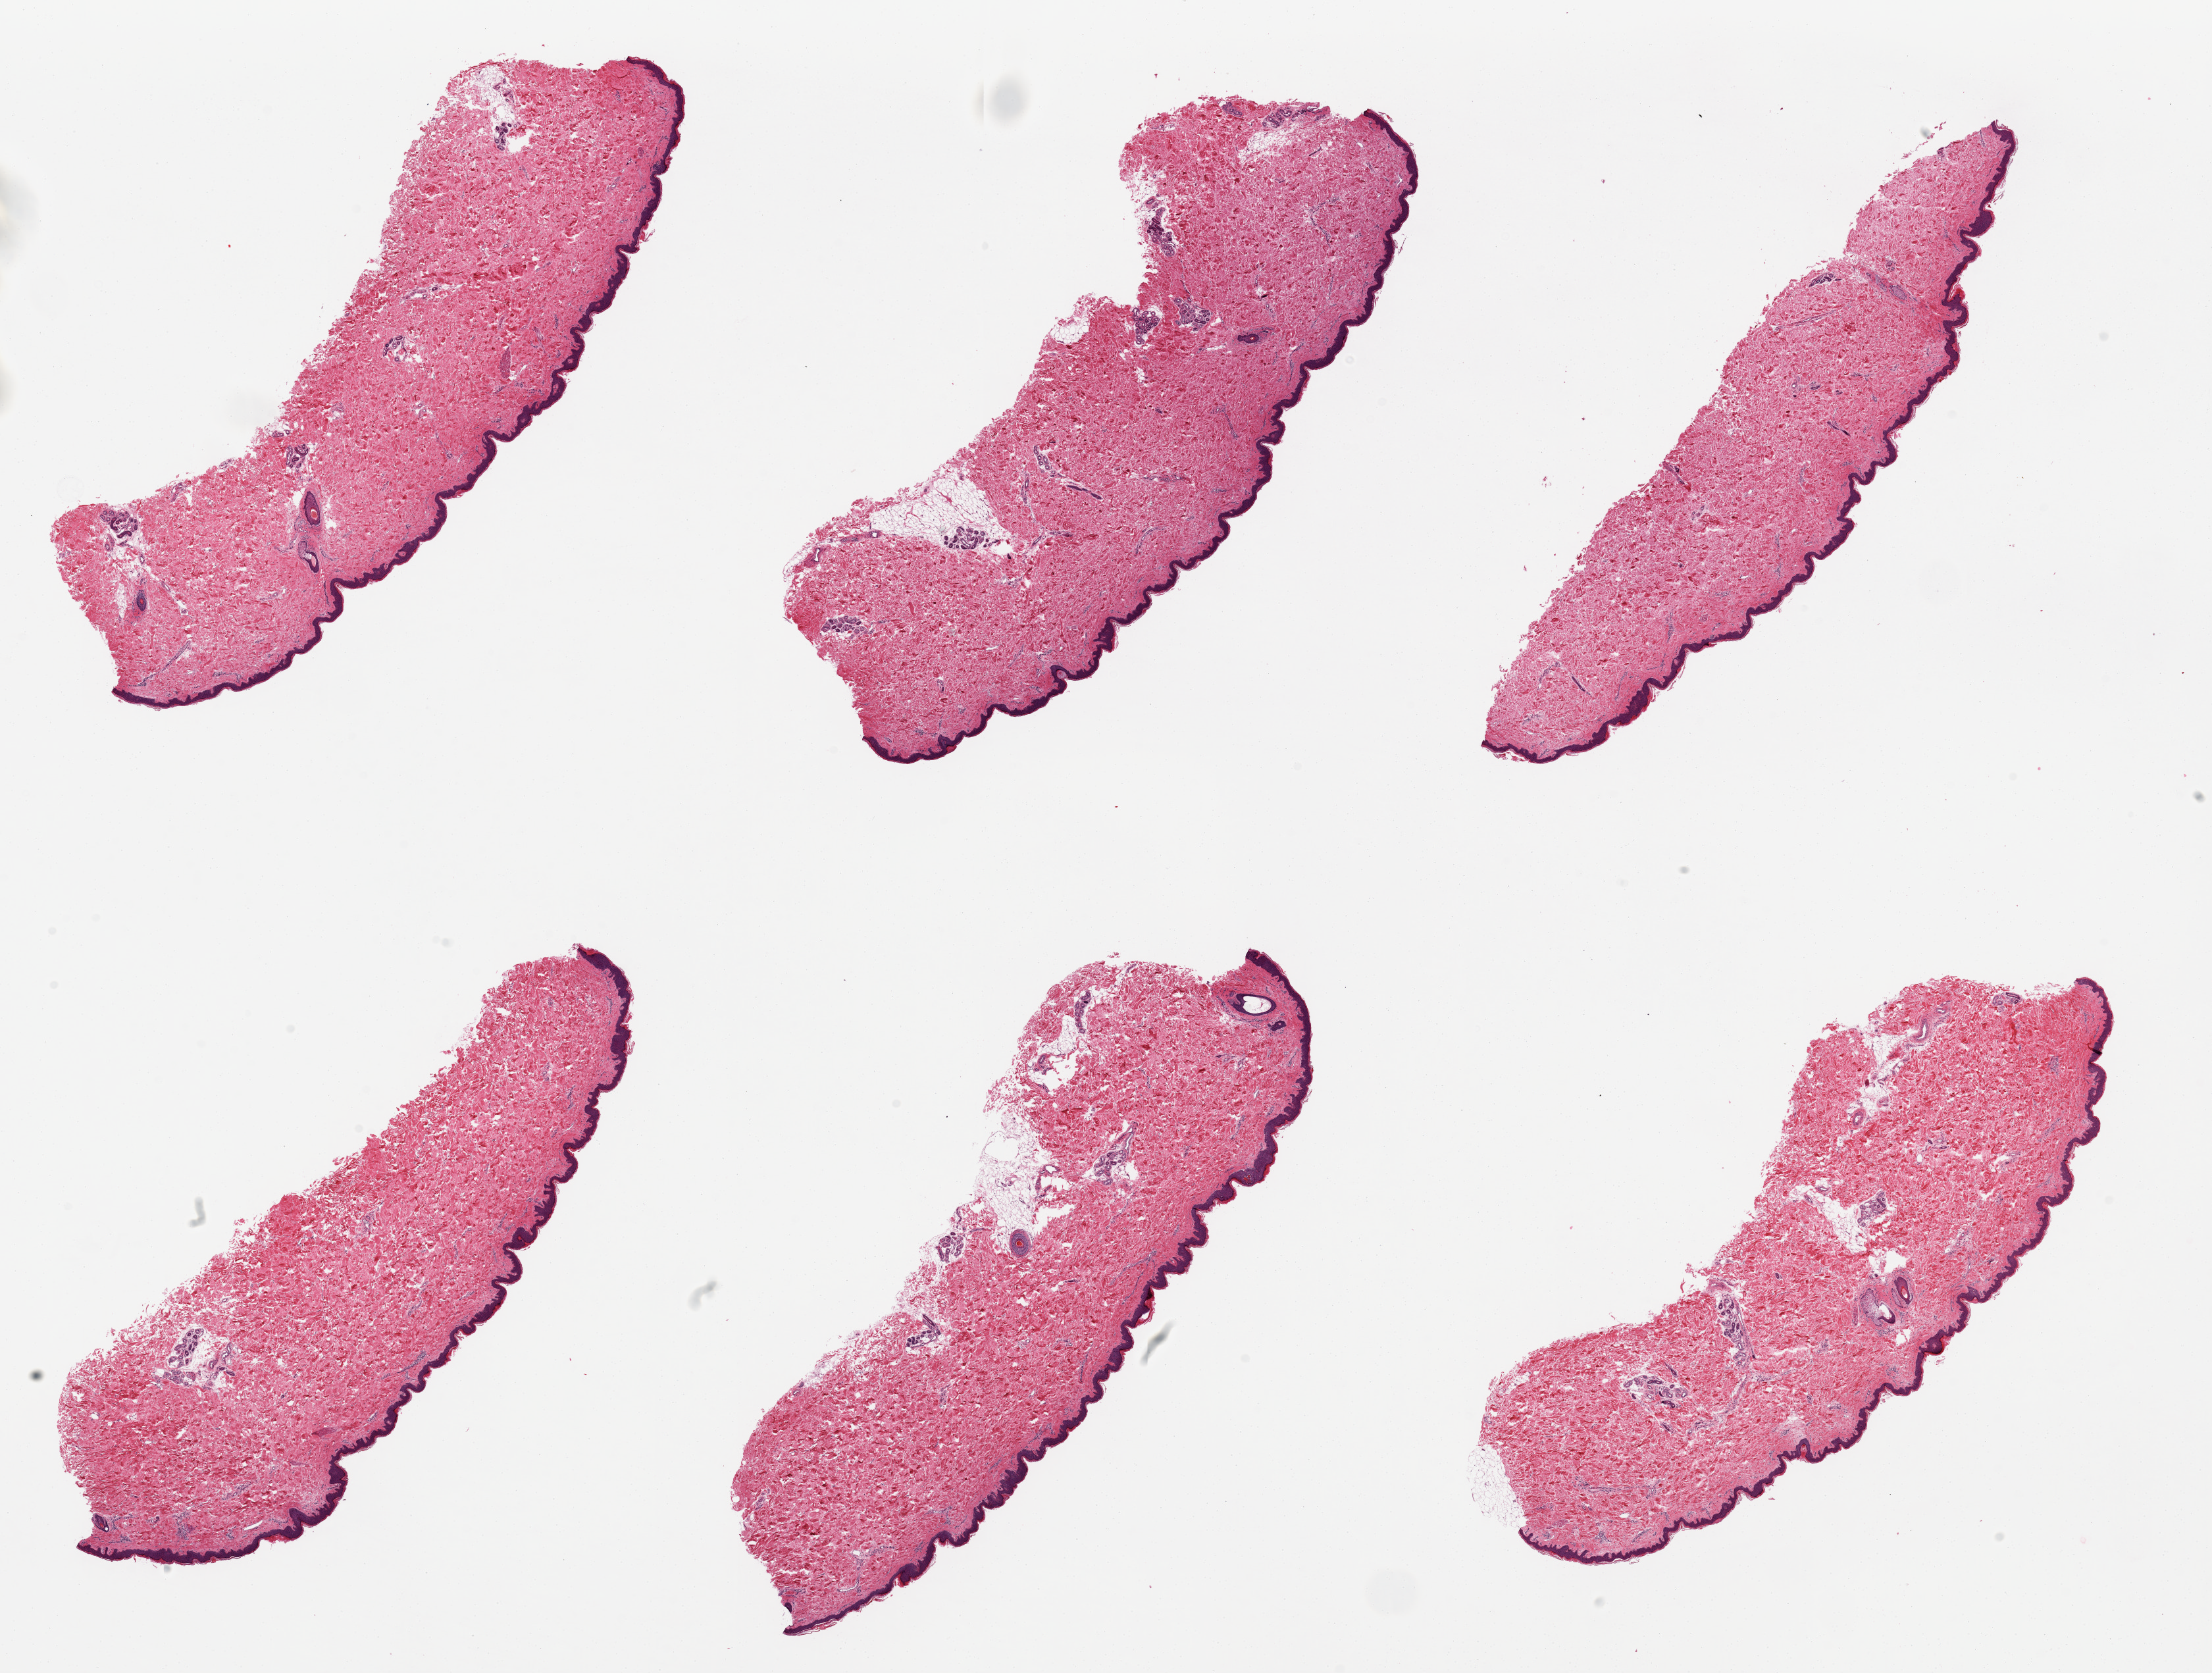
Whole-slide image, haematoxylin and eosin stain, brightfield — a low-resolution overview of the entire scanned area, about 26.6 x 20.1 mm. PAXgene-fixed paraffin-embedded (PFPE) section. Sampled site (target tissue): skin of lower leg. Tissue donor sample. Donor sex: male.
Review note (as recorded): 1 piece 5x3mm; well trimmed.